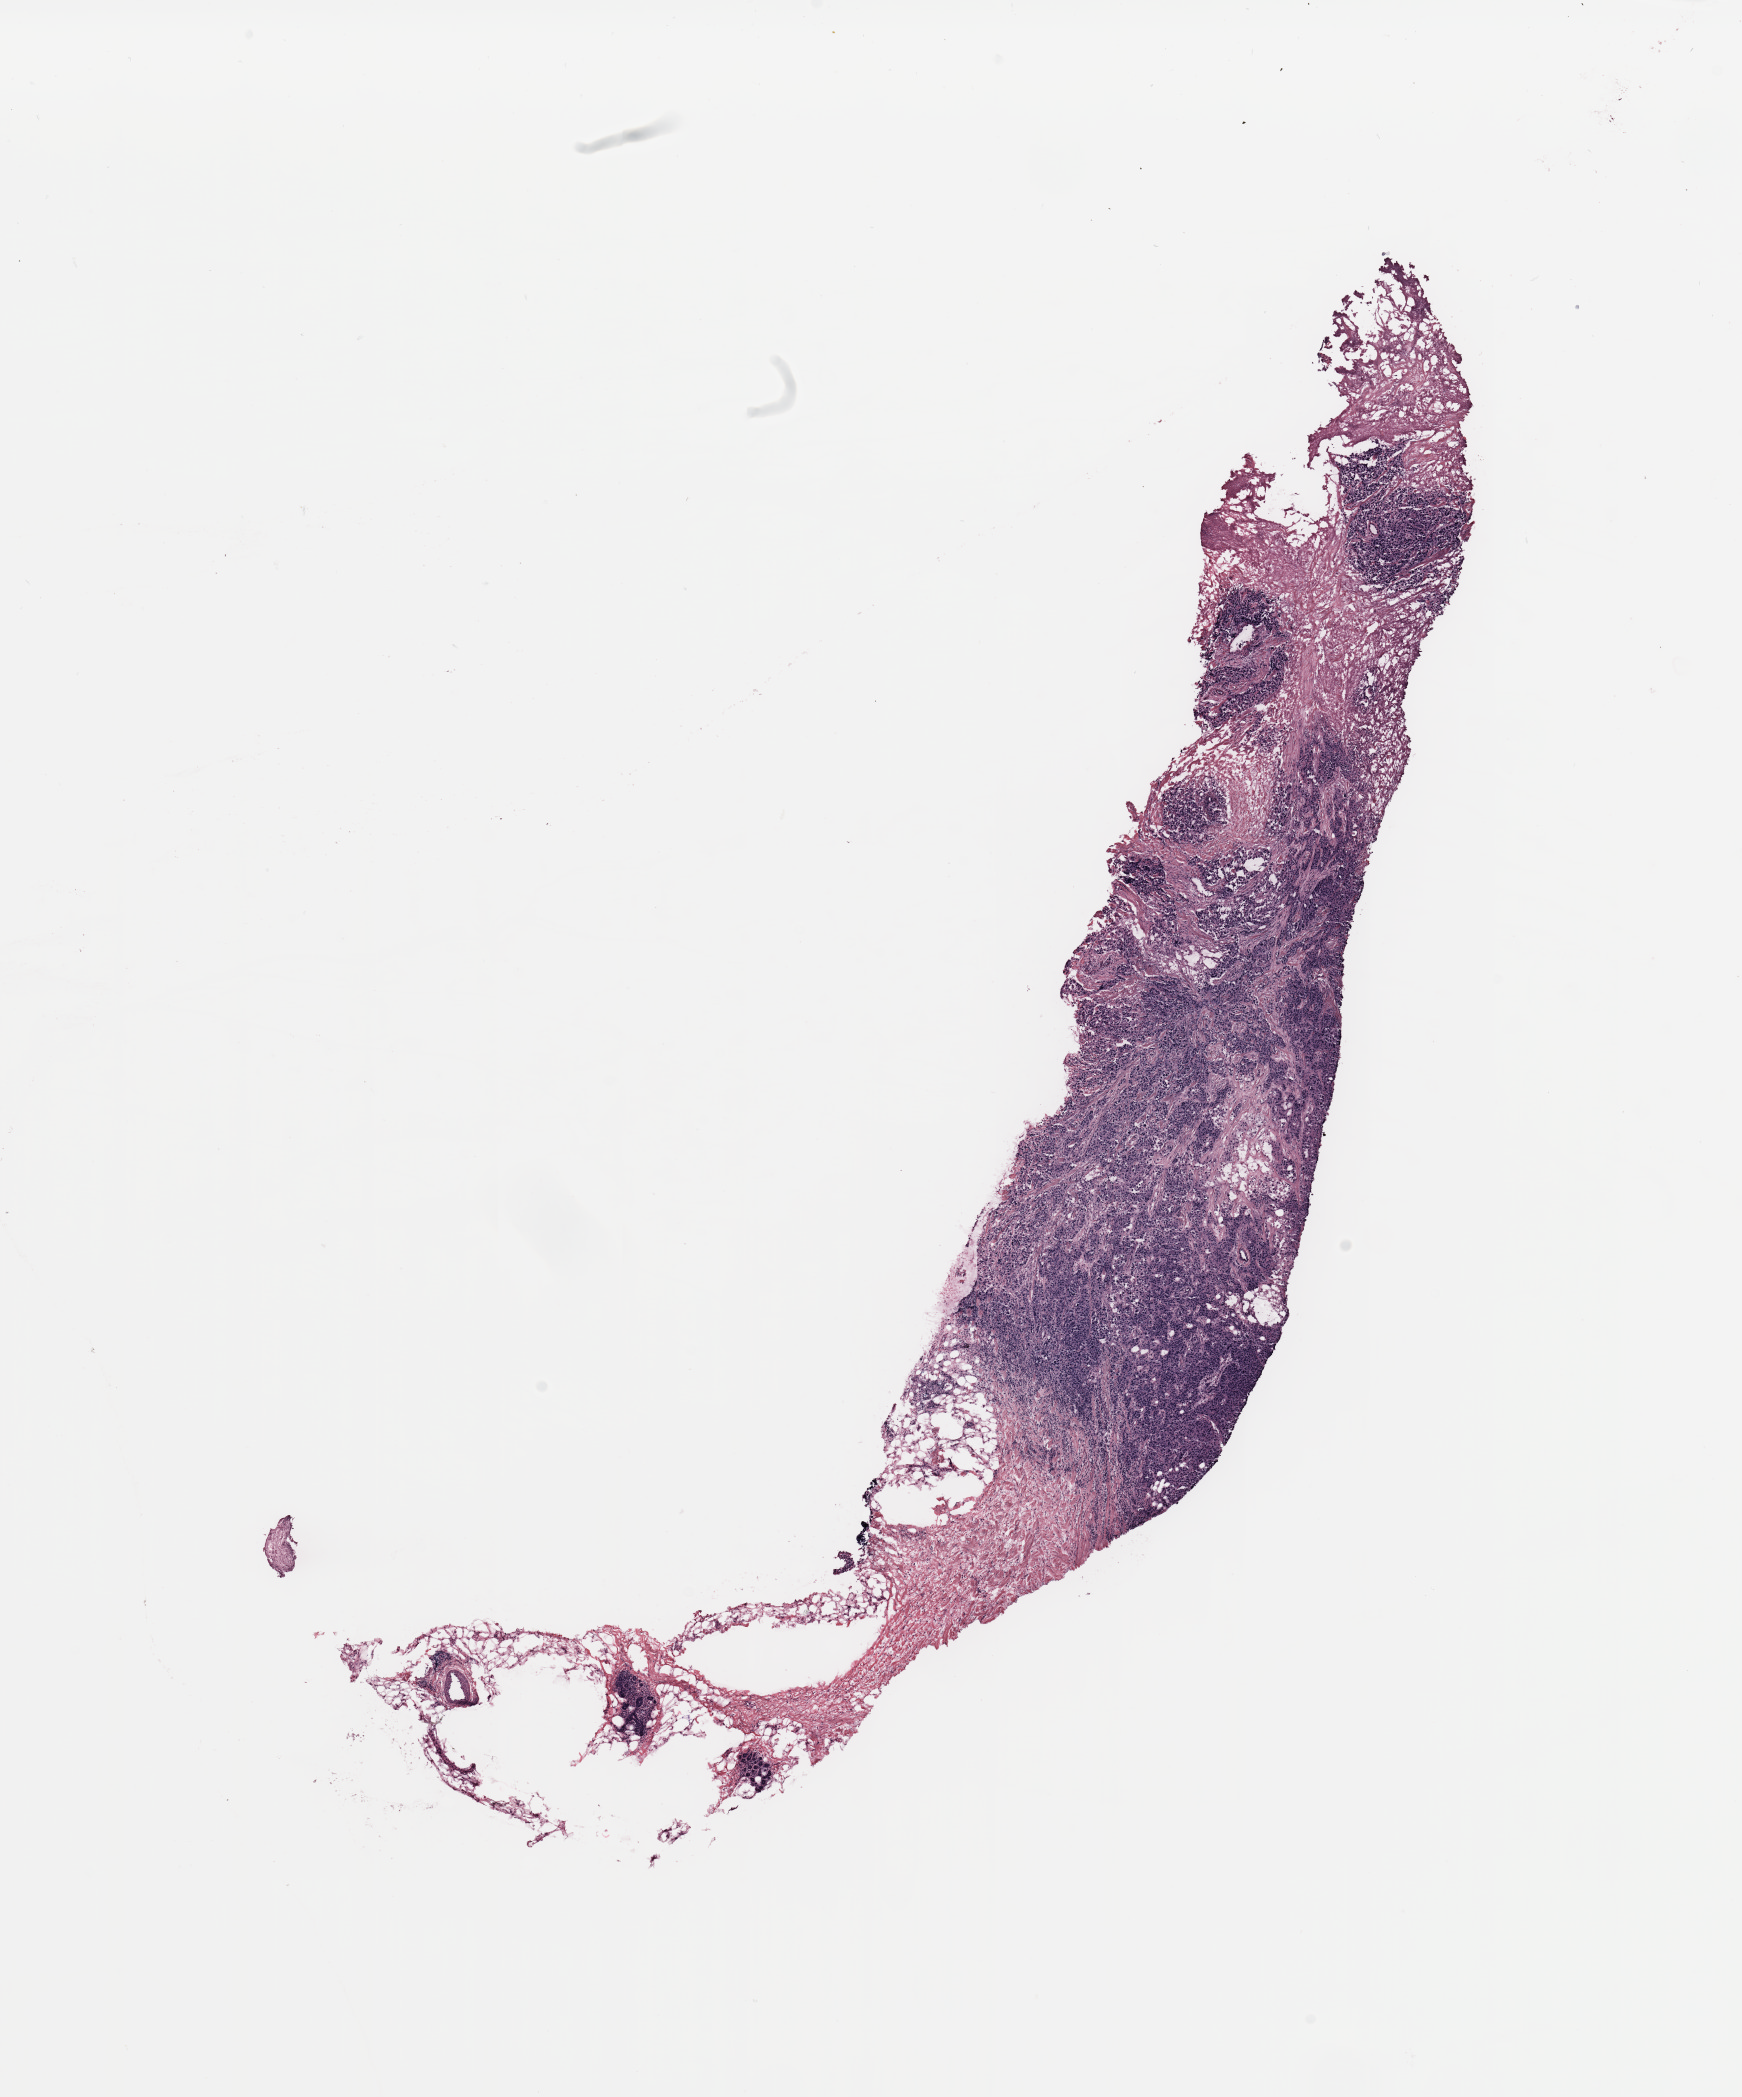
Whole-slide histology image, H&E — a low-resolution overview of the entire scanned area, about 13.8 x 16.6 mm (acquisition: 20x scan); breast, tissue type not recorded.
- patient diagnosis (cohort enrolment): breast cancer (breast)